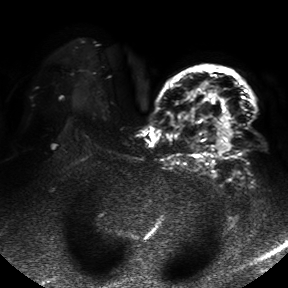
Breast MRI, one axial slice. Slice 32 of 50 in the series (ordered by position). Diffusion-weighted series; image 2 of 4 stored at this slice position (different b-values; order by instance number). 1.5 T. 4 mm slice thickness. 288 × 288 image matrix, field of view 390 × 390 mm. Female patient.
Outlined on this slice (expert manual segmentation):
- tumour on diffusion-weighted imaging: bounding box [x1, y1, x2, y2] px = [216, 110, 233, 153]